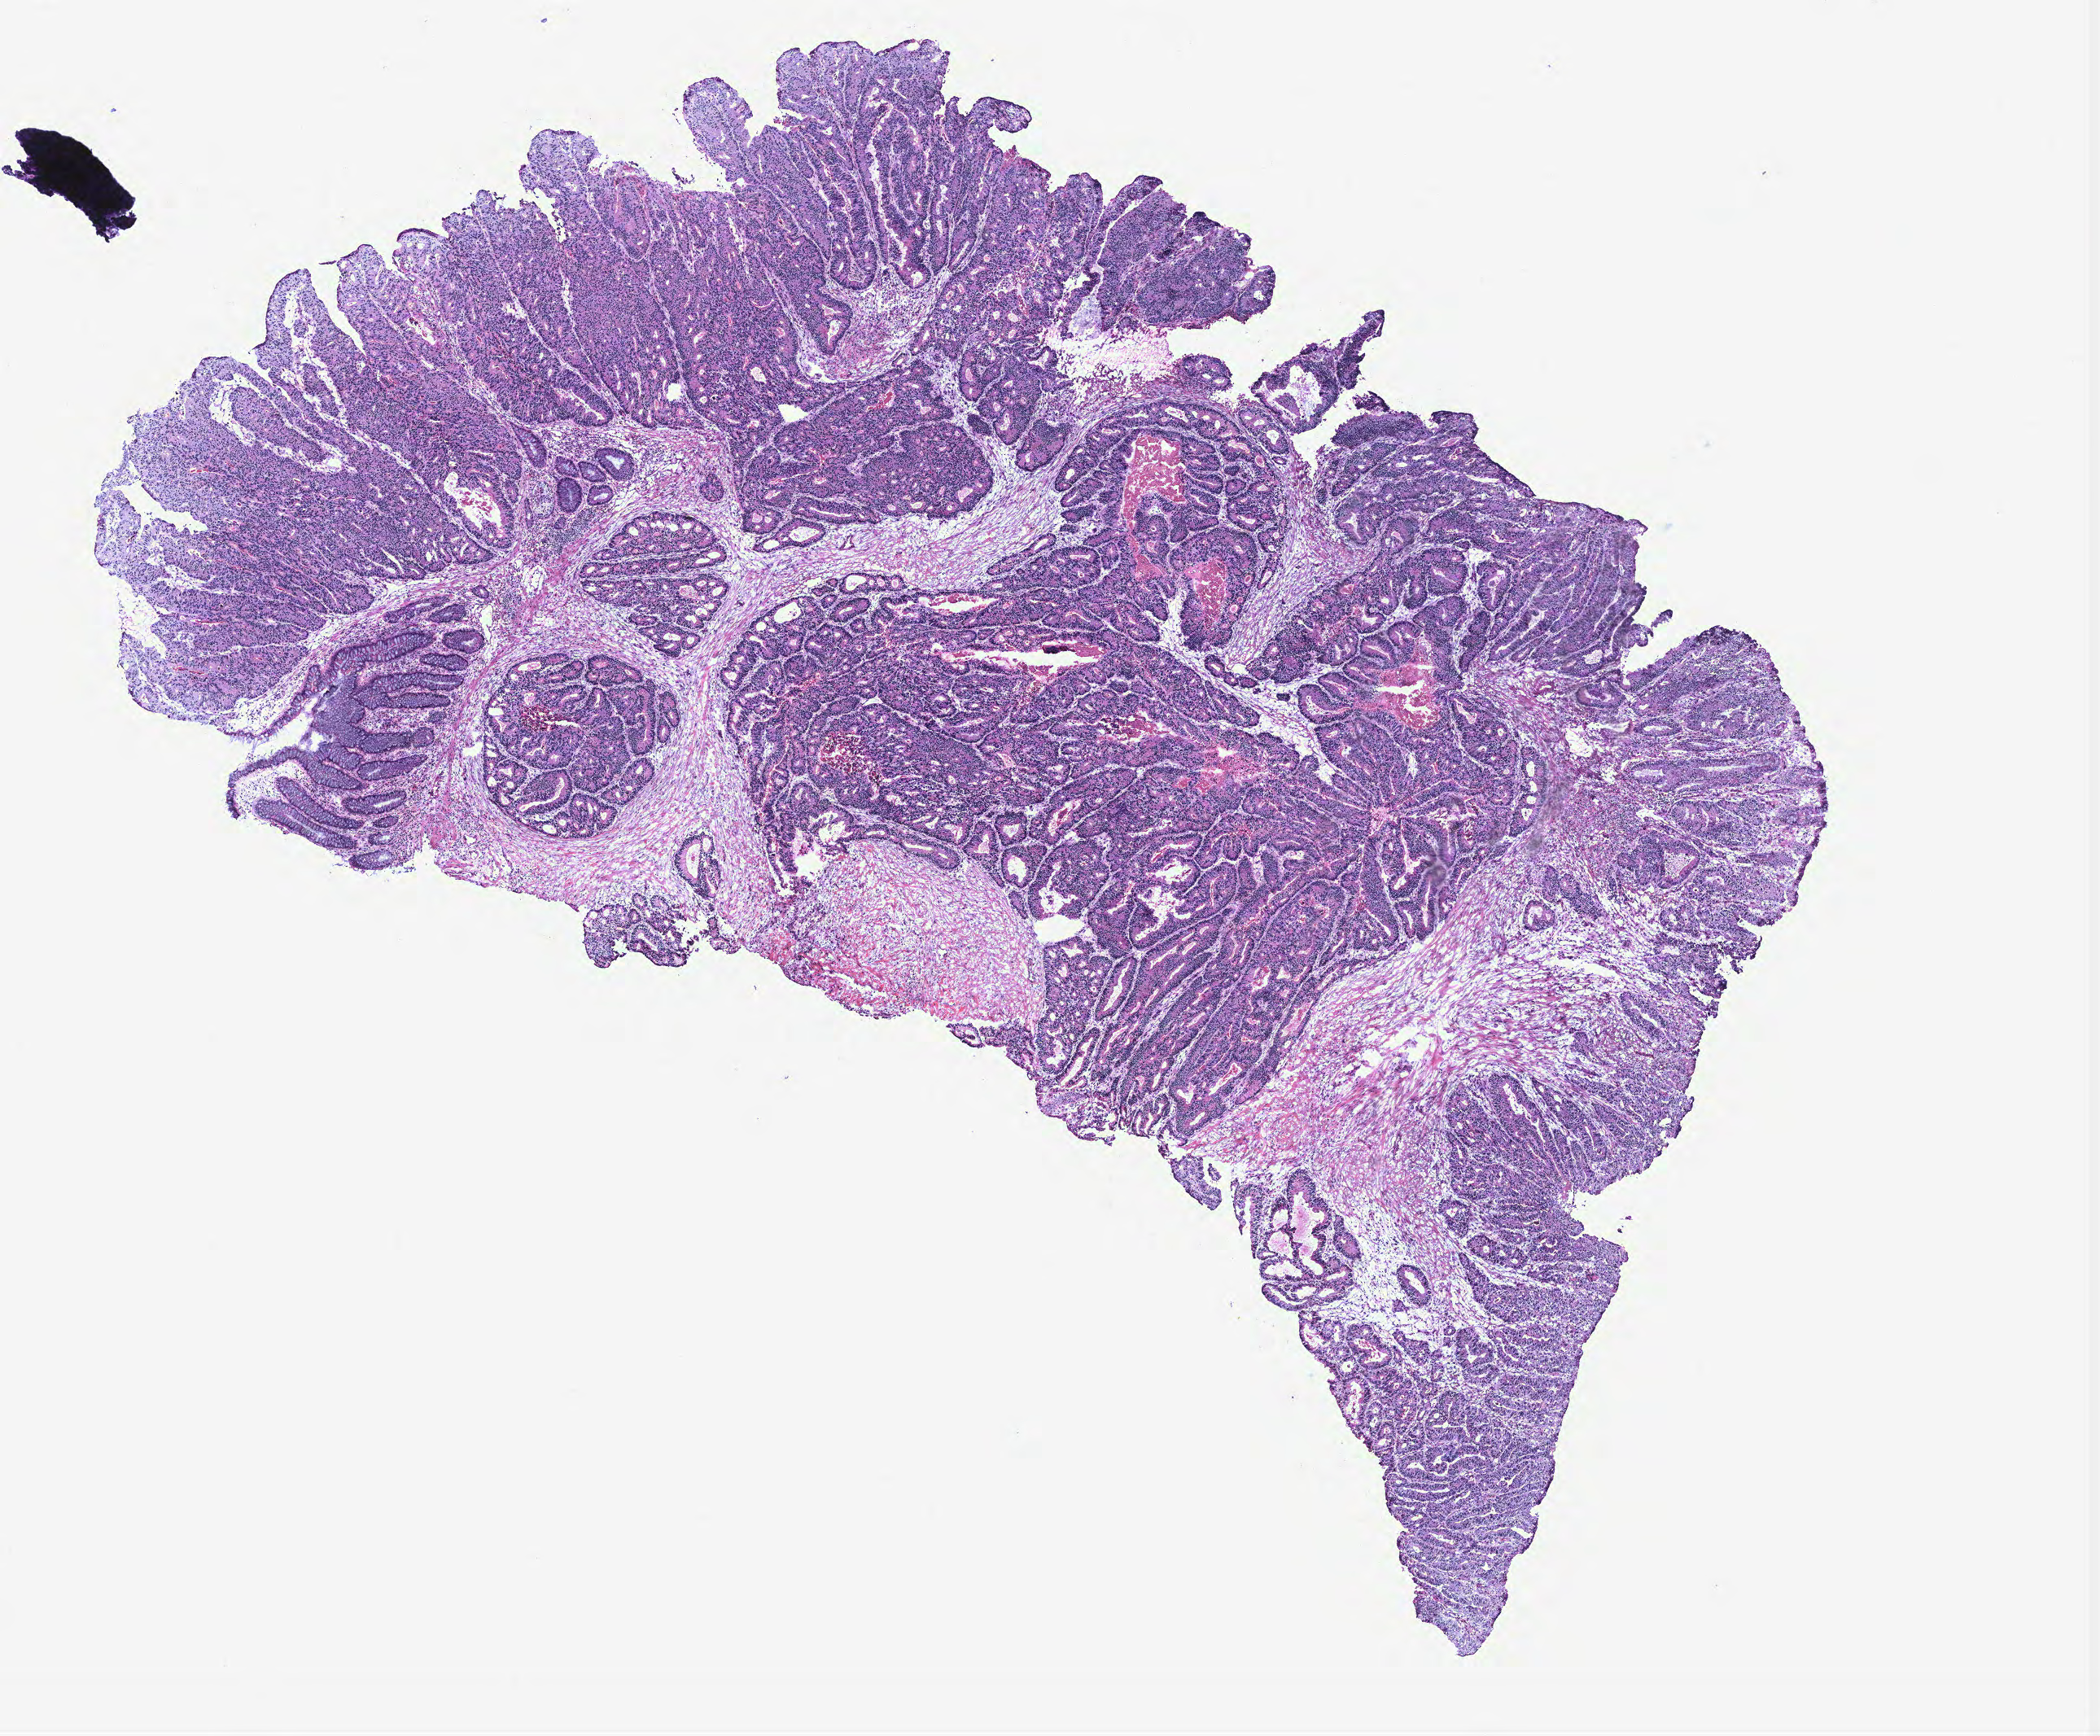
Digitized H&E tissue section (whole slide) — shown as a low-resolution overview of the whole scanned area (about 10.3 x 8.5 mm), colon, tissue type not recorded.
Patient diagnosis (cohort enrolment): colon cancer (colon).